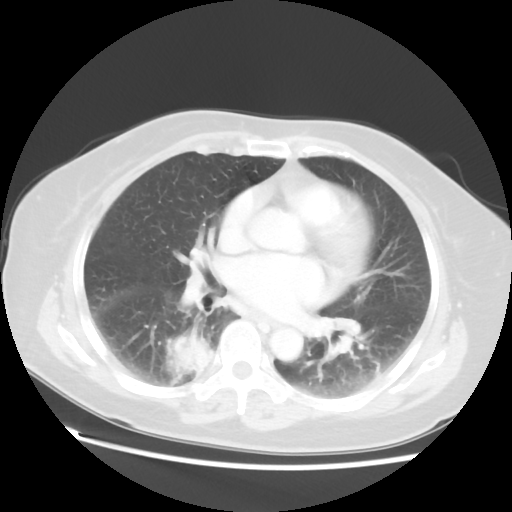
Chest CT, one axial slice; position 28 of 52 along the scan axis; lung window (W 1500 / L -600 HU); 5 mm slice thickness; 512 × 512 image matrix, field of view 356 × 356 mm. Patient: female, 69 years. Case-level facts recorded for this patient, not image findings: clinical TNM (as recorded): T2 N1 M1a.
Outlined on this slice (rectangle marked by the reading radiologist):
- lung tumour (recorded histology: adenocarcinoma): bounding box <166,328,214,376> (left, top, right, bottom; pixels)